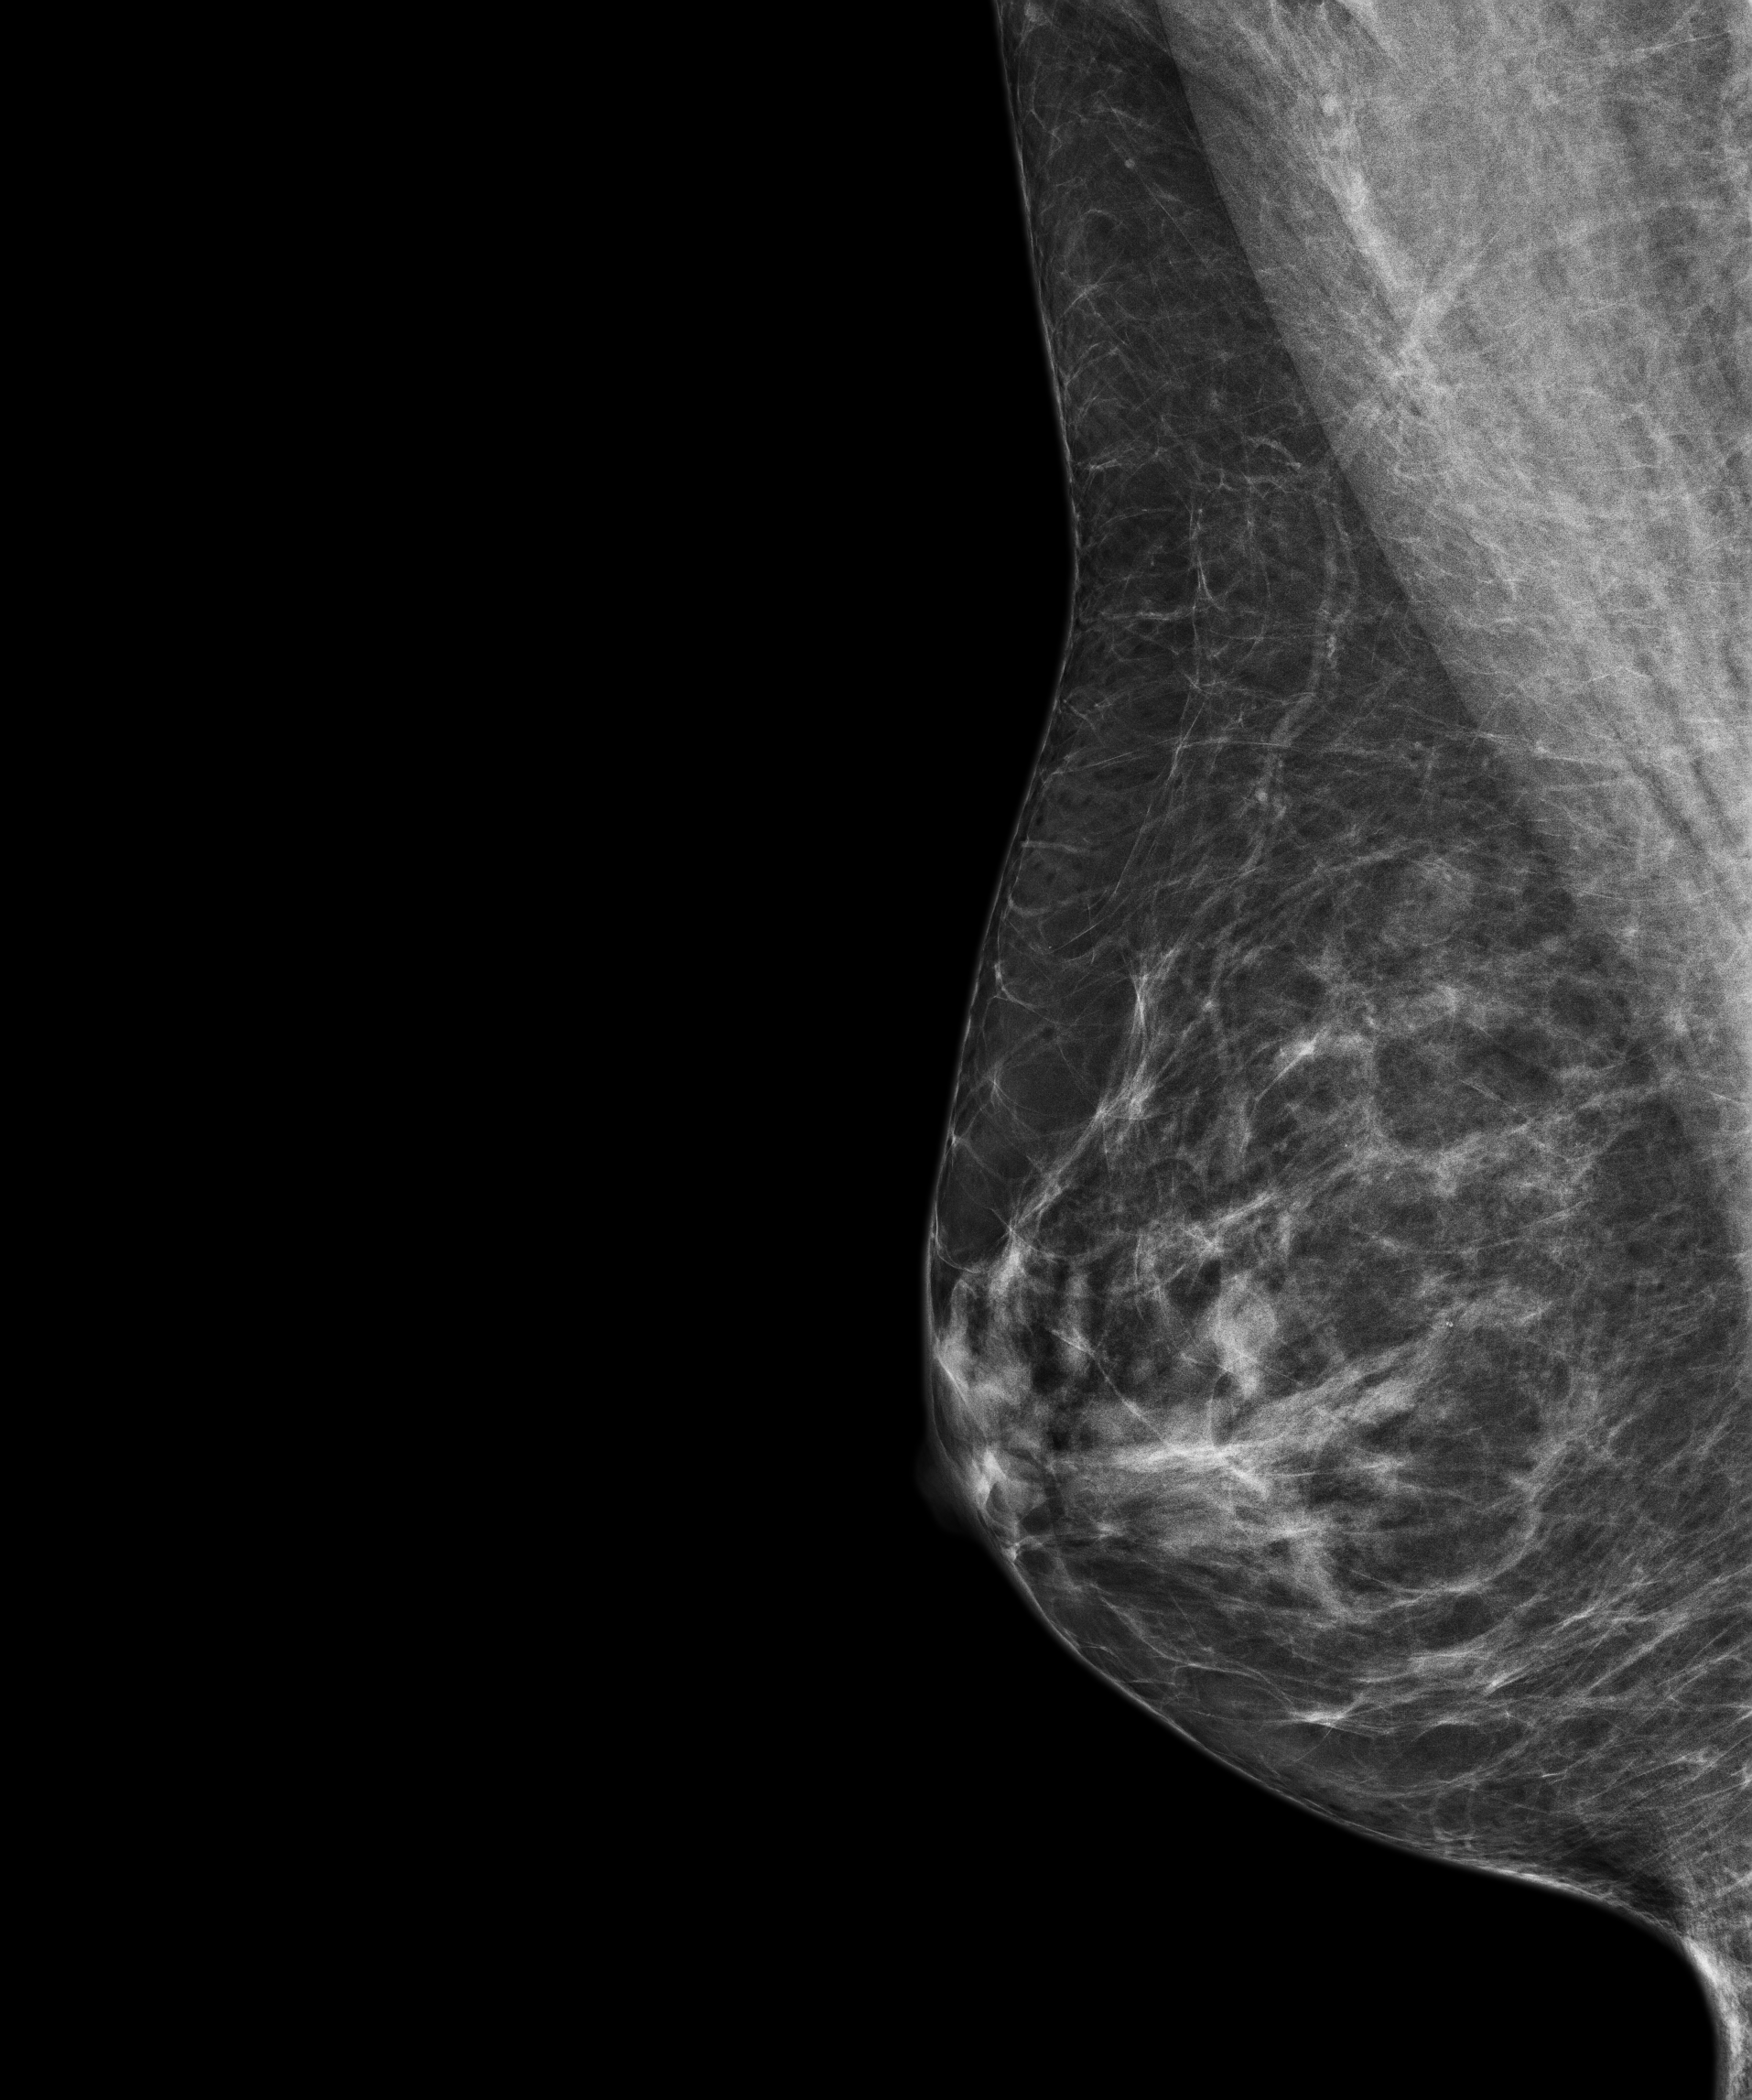
Annual screening mammography examination; compressed breast thickness 54.1 mm; system: Senographe Pristina. Female patient, age 58 years.
Image type: full-field digital mammogram. Breast: right. Projection: mediolateral oblique (MLO) view.